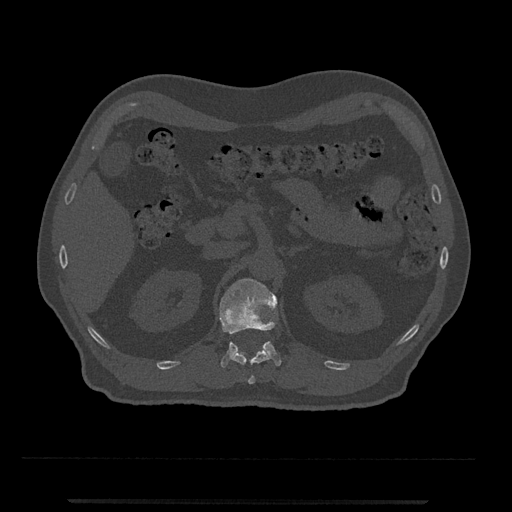
CT including the spine, one axial slice. Position 366 of 797 along the scan axis. Reconstruction kernel Br40s/3. 120 kVp. Bone window (W 1800 / L 400 HU). 0.5 mm slice thickness. 512 × 512 image matrix, field of view 419 × 419 mm. Male patient, age 63 years. From the clinical record (not read from this slice): primary cancer: prostate.
Annotated regions visible in this slice (semi-automatically segmented with operator editing):
- L1 vertebra: bounding box <219,278,281,368> (left, top, right, bottom; pixels)
- T12 vertebra: <231,348,270,384>